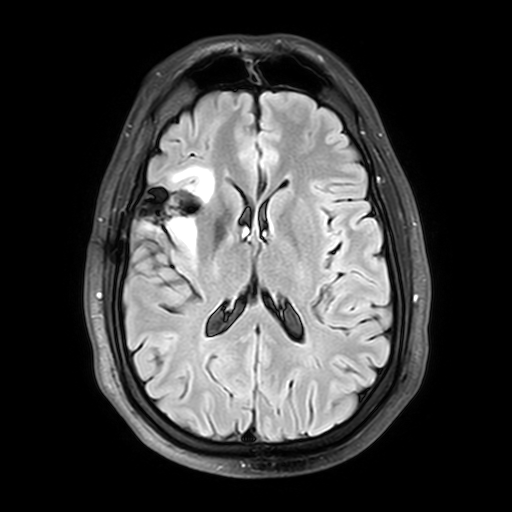
Brain MRI from a brain-tumour surgery series, one axial slice; slice 19 of 42 in the series (ordered by position); T2 FLAIR; 4 mm slice thickness; 512 × 512 image matrix, field of view 240 × 240 mm. From the clinical record (not read from this slice): histopathology: Astrocytoma; WHO grade: 2; IDH mutation: yes; tumour location: Right Insular.
Annotated regions visible in this slice (outlined manually by an expert reader):
- tumour: bounding box (x1, y1, x2, y2) in pixels: (137, 167, 223, 254)